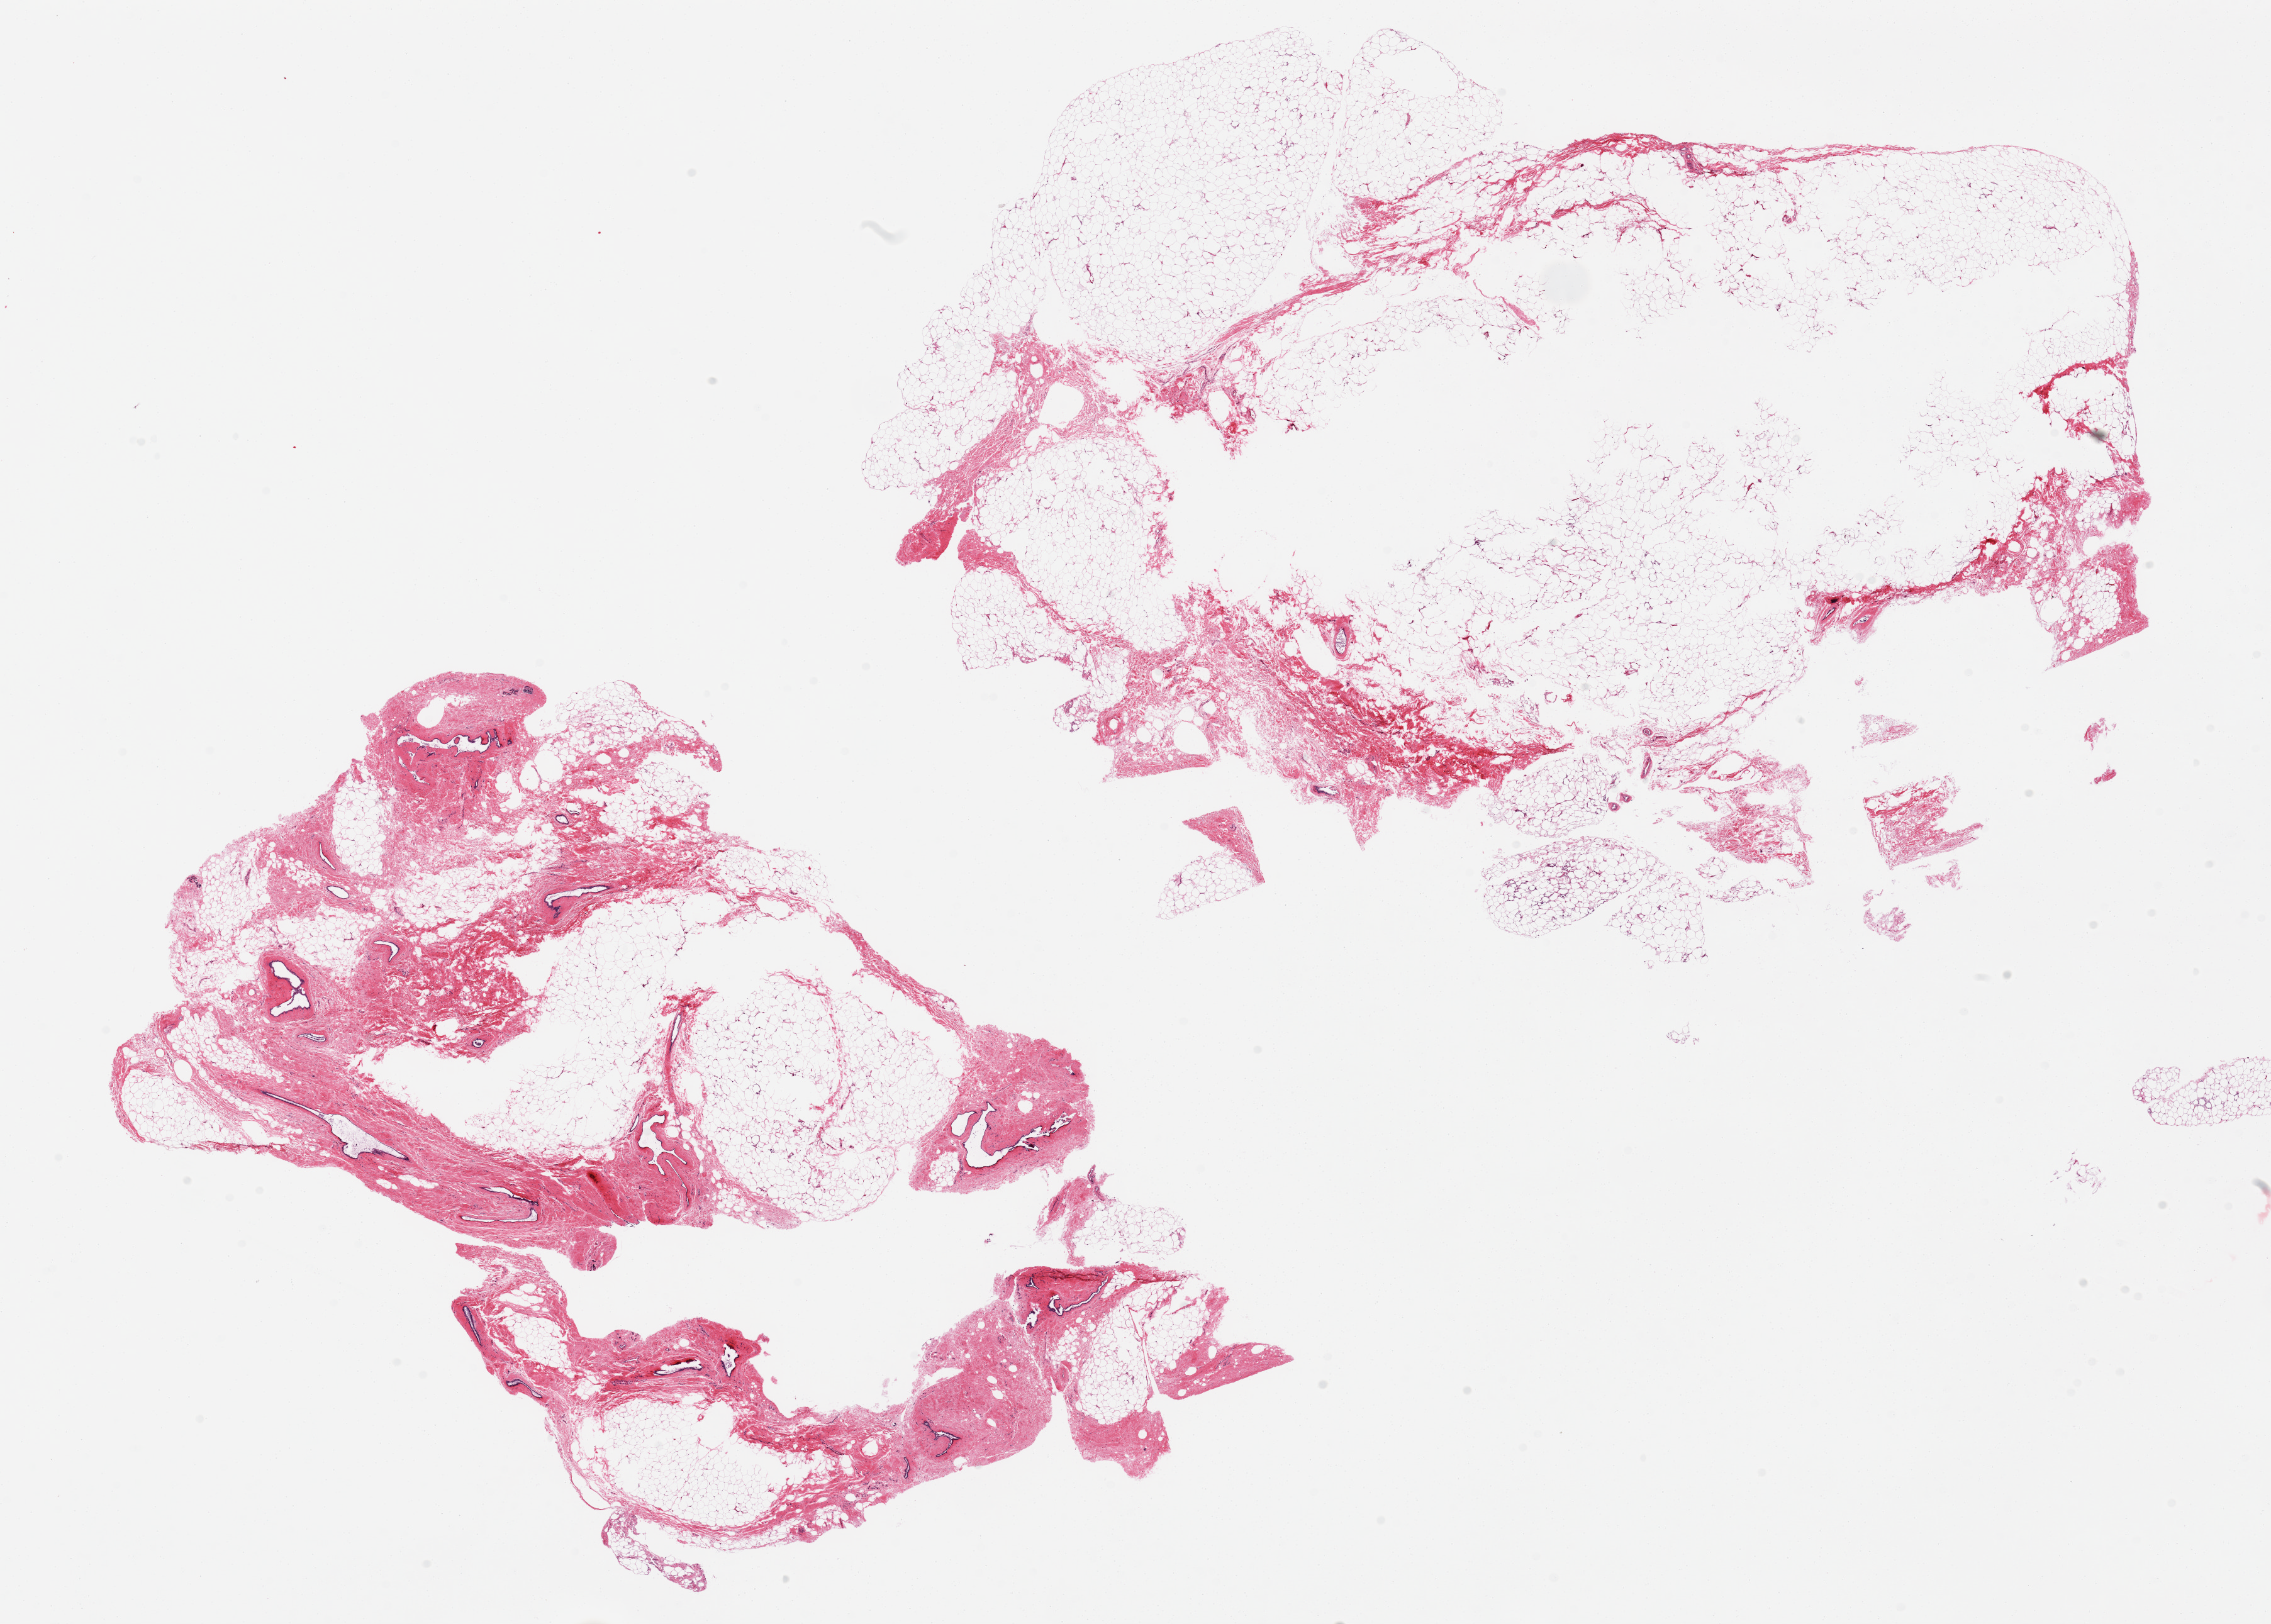
Hematoxylin and eosin (H&E) whole-slide image — shown as a low-resolution overview of the whole scanned area (about 28.5 x 20.4 mm), PAXgene-fixed paraffin-embedded (PFPE) section, section of breast (target tissue), tissue donor sample. Male donor.
Reviewer comment on this tissue sample: 2 pieces; ducts present, especially in 1 piece.